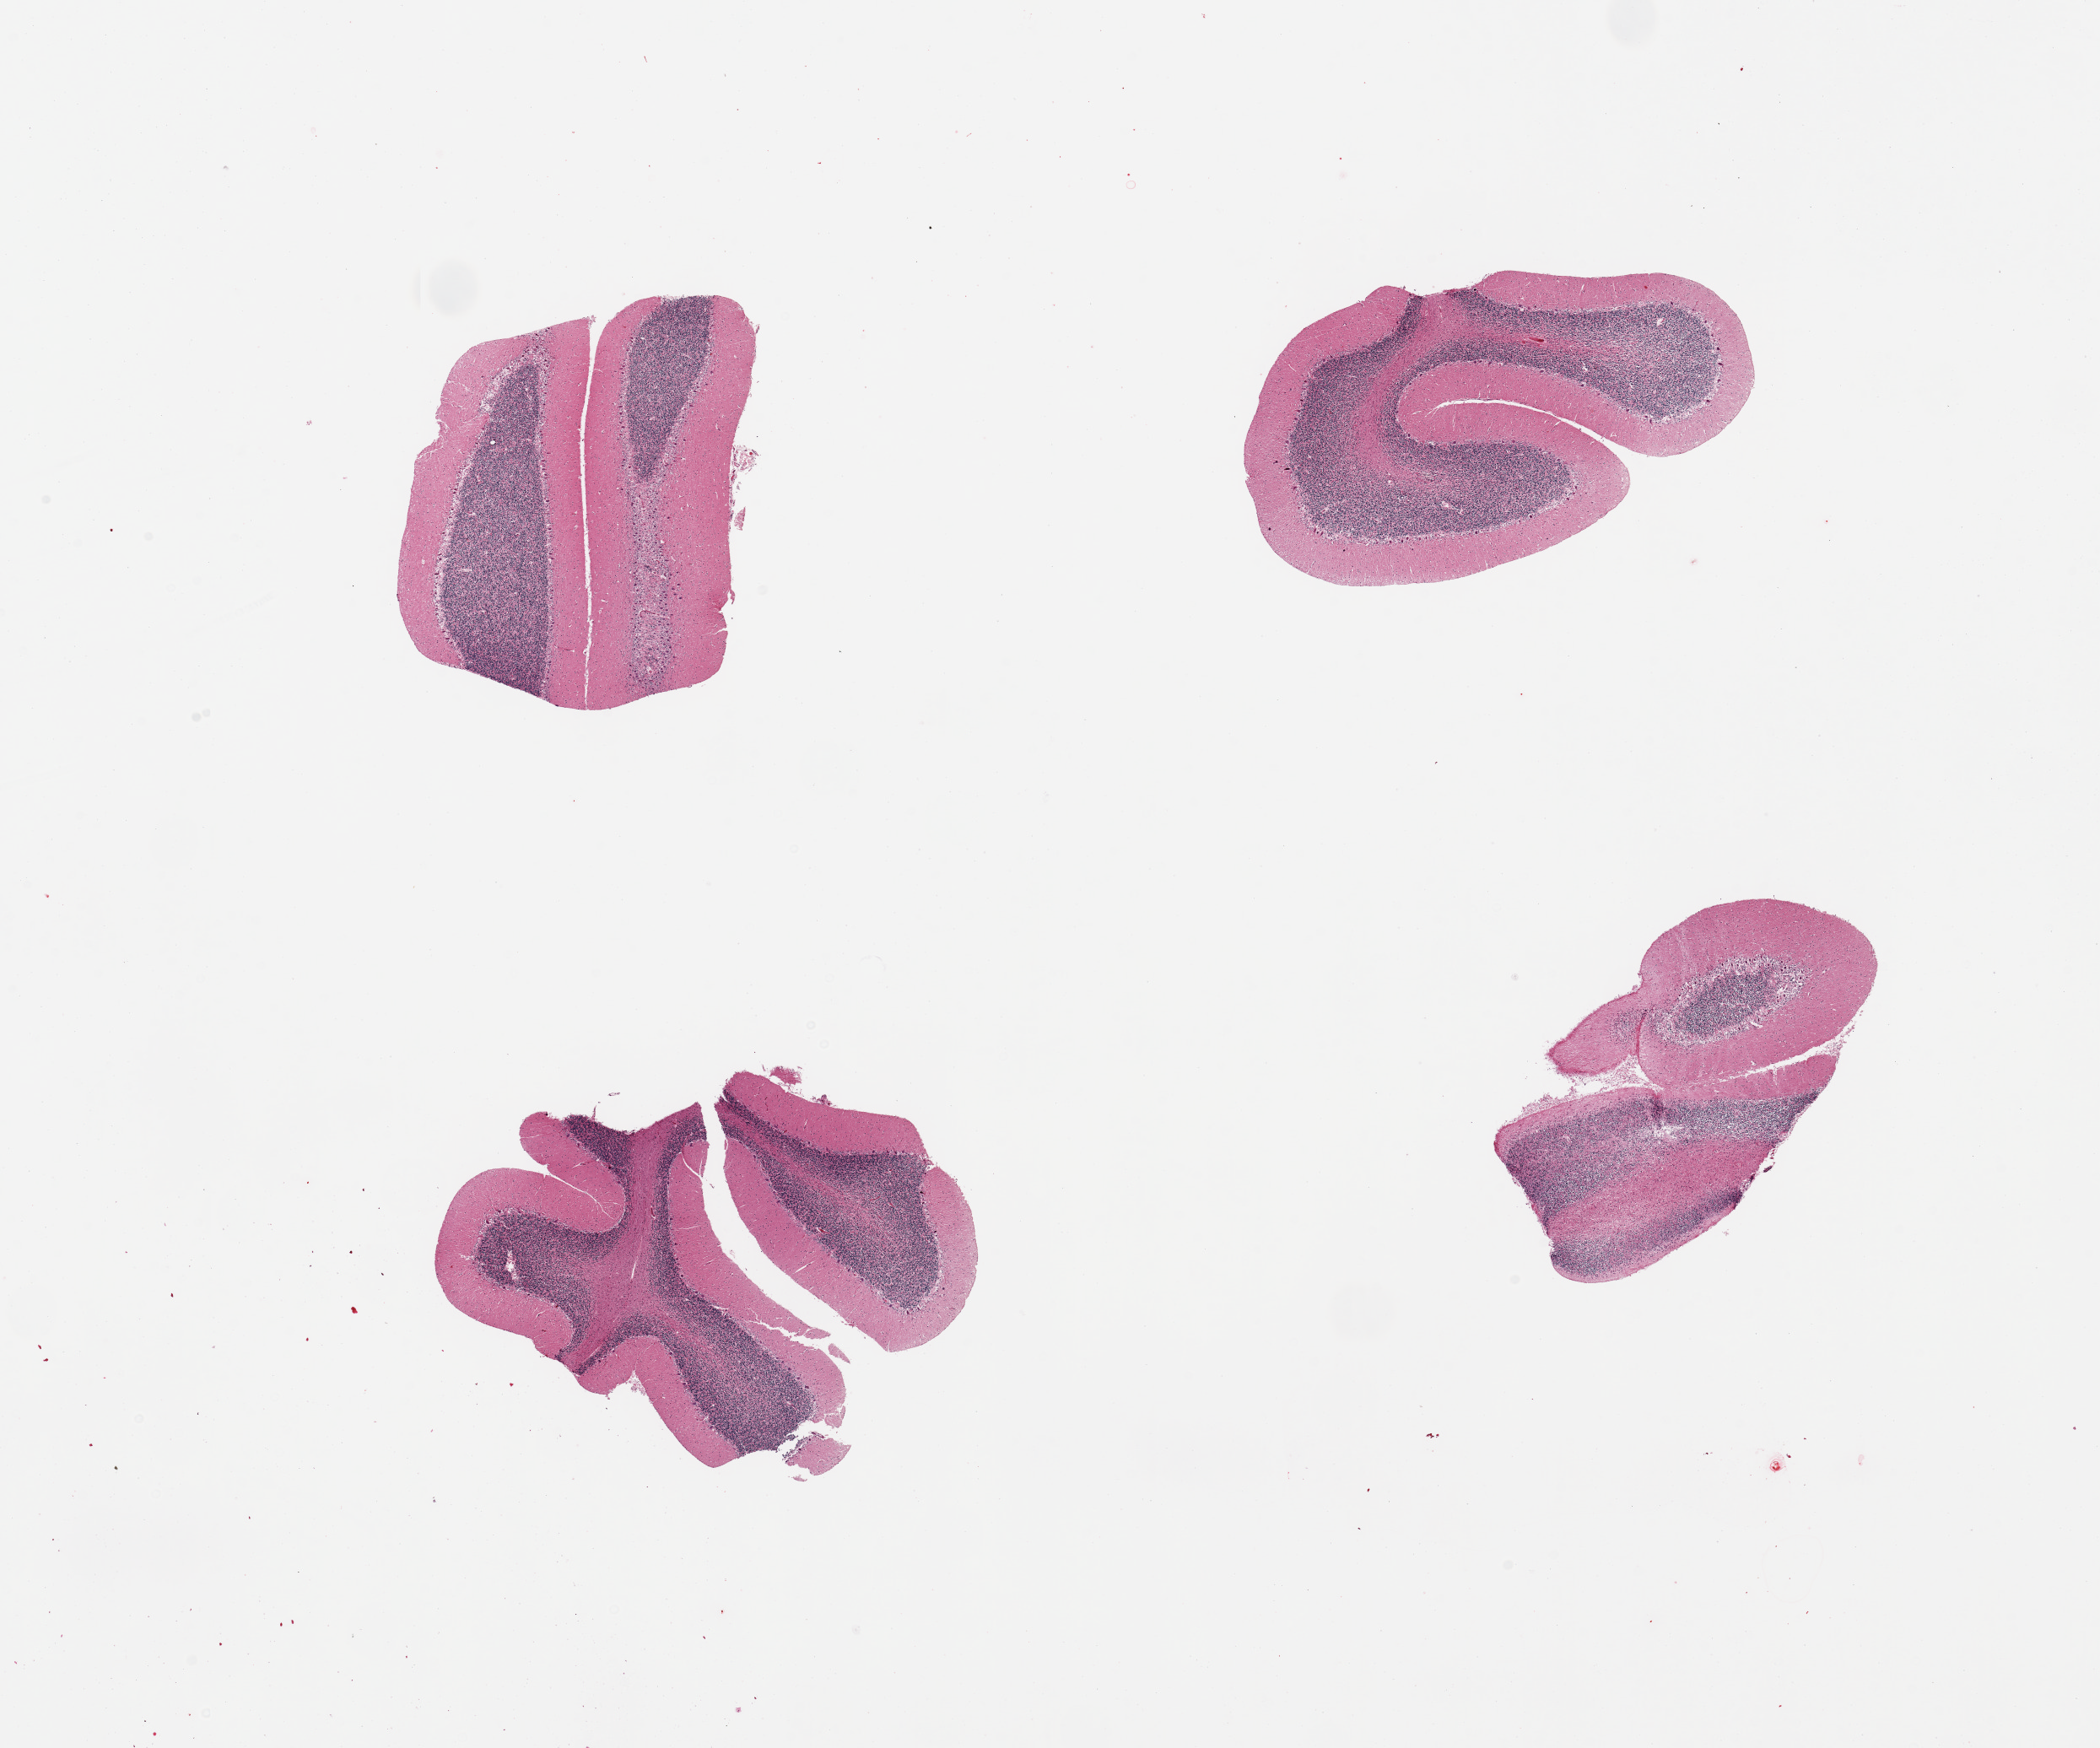
Hematoxylin and eosin (H&E) whole-slide image — a low-resolution overview of the entire scanned area, about 19.7 x 16.4 mm (from a 20x scan). PAXgene-fixed paraffin-embedded (PFPE) section. Sampled site (target tissue): cerebellum. Donor tissue sample. Donor: male.
Pathologist's review note for this sample: 4 pieces.